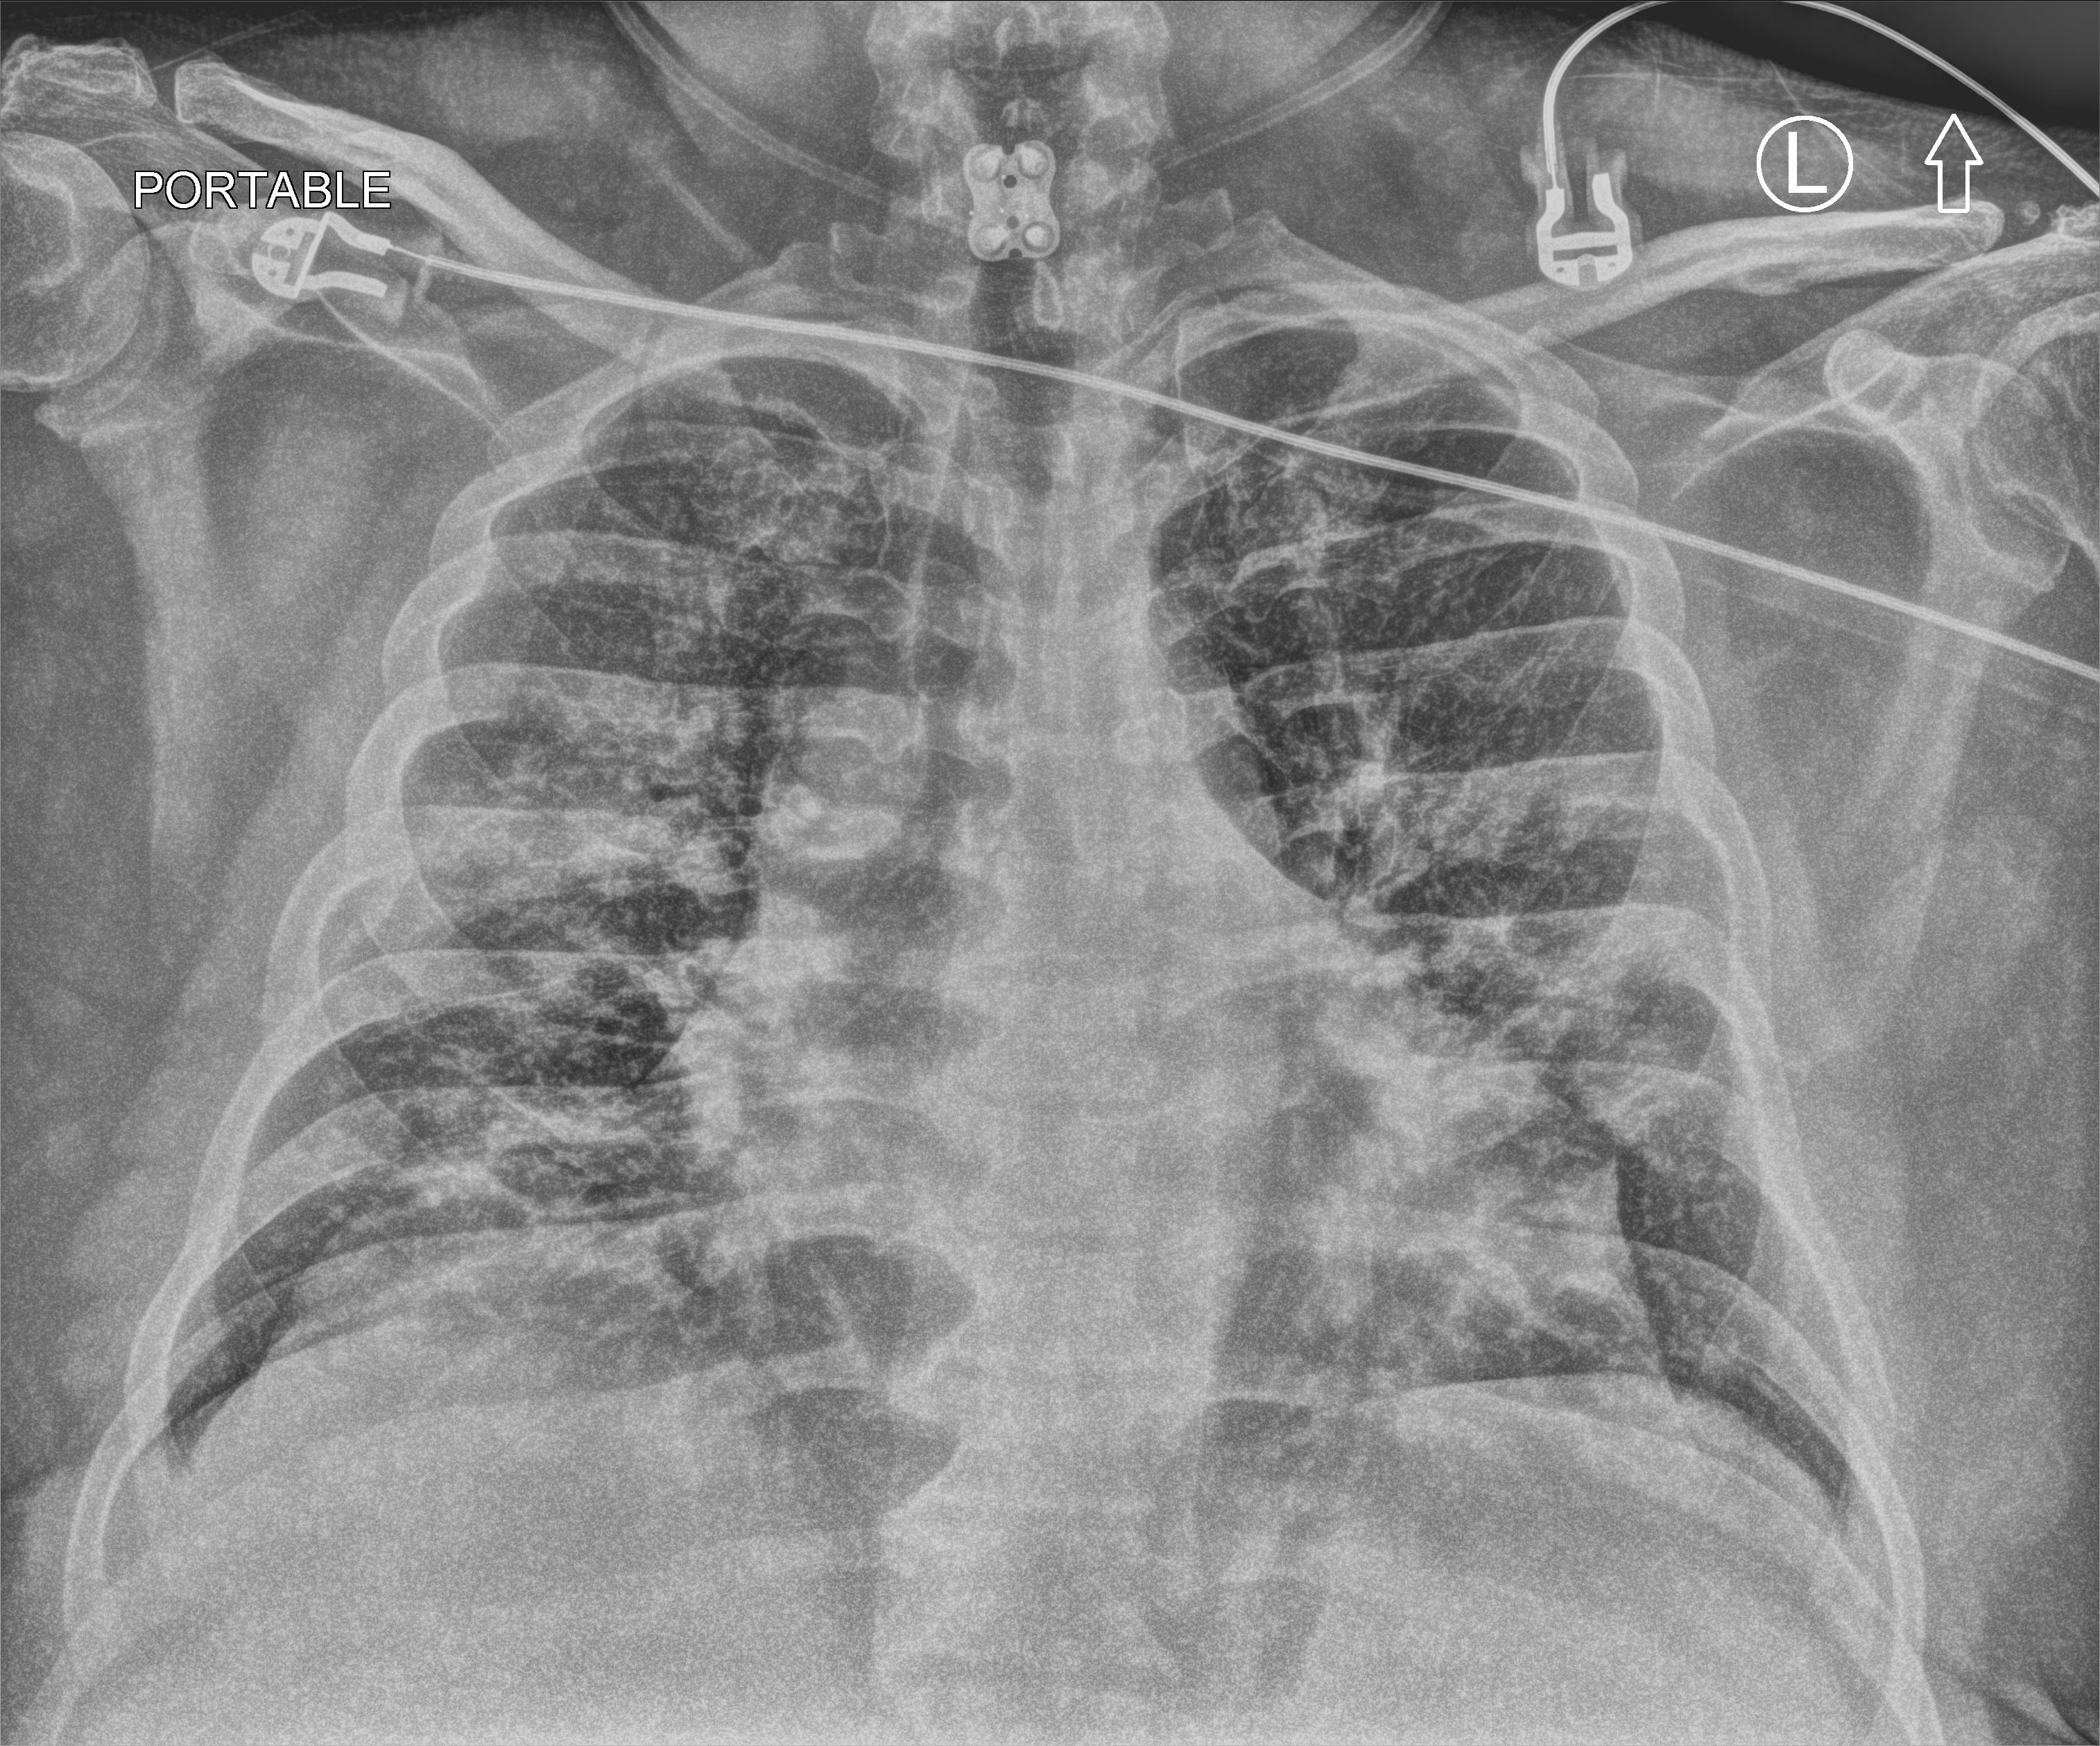
Chest X-ray (portable), anteroposterior (AP) projection. Male patient hospitalised with COVID-19, age 18–59 years.
From the hospital-stay record, not from the radiograph (when in the stay this image was taken is not recorded):
- mechanically ventilated during this hospital stay: yes